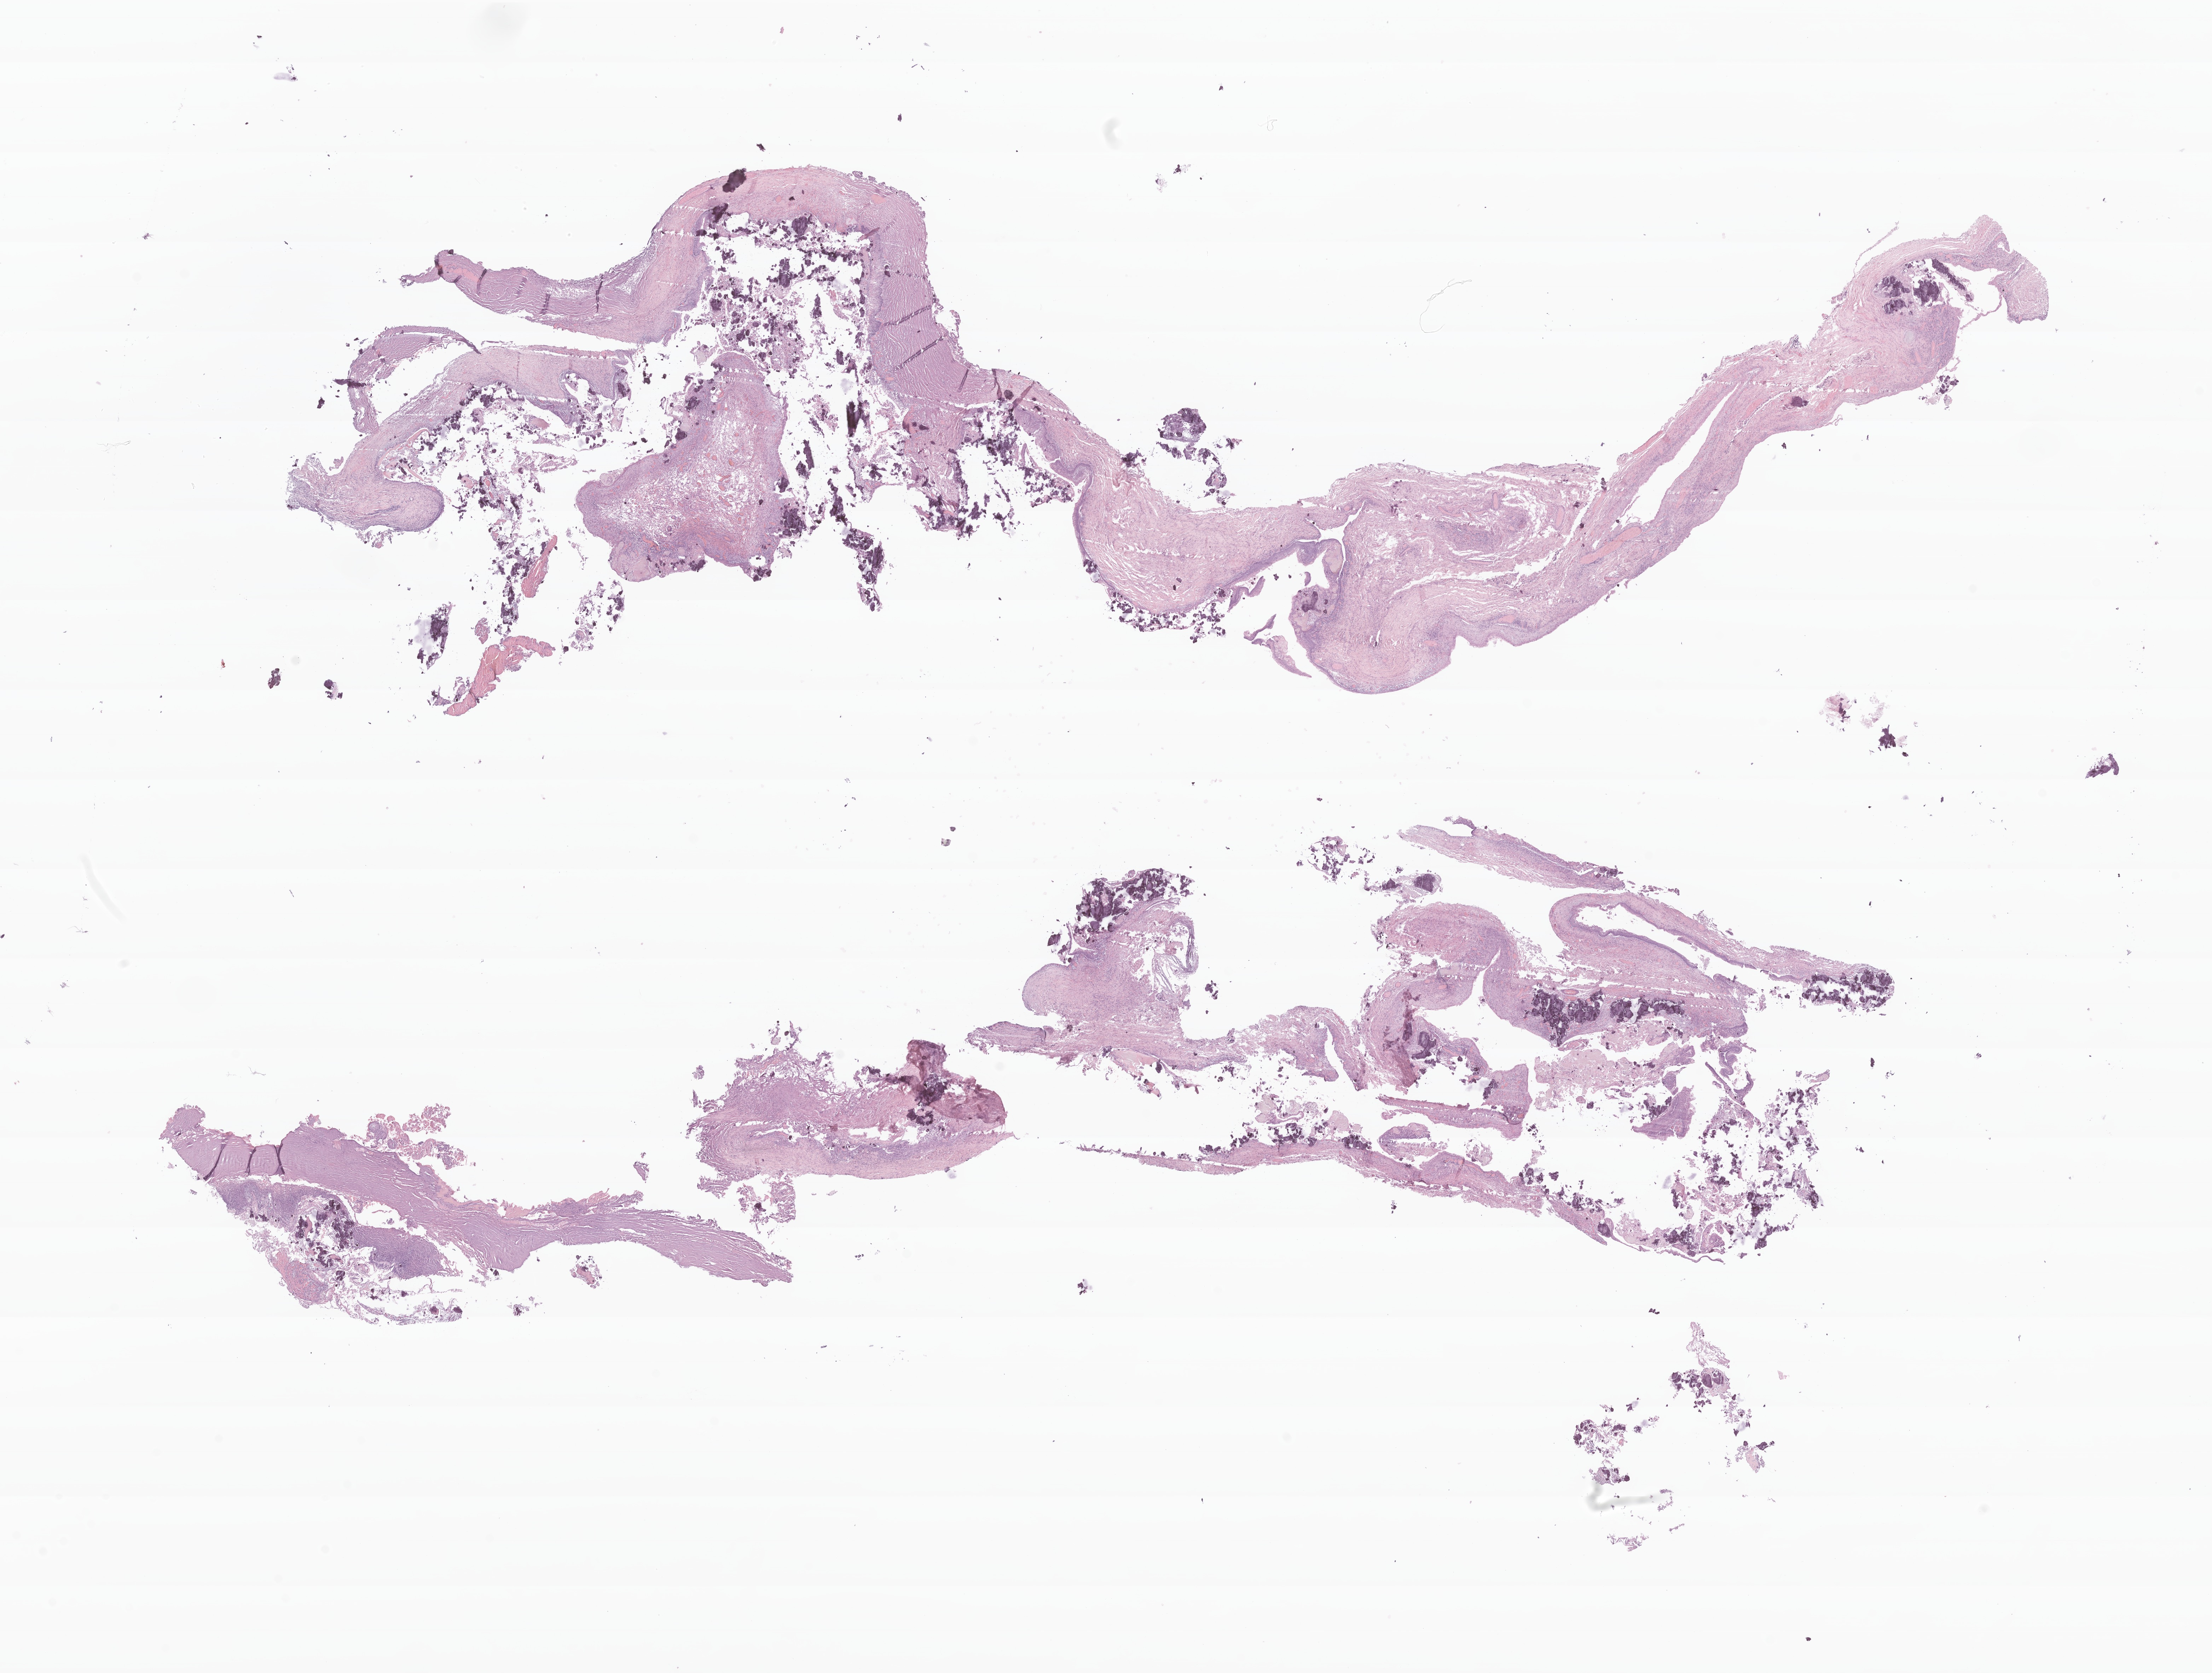
Whole-slide image, haematoxylin and eosin stain of tumor tissue from the brain, shown as a low-resolution overview of the whole scanned area (about 26.3 x 19.9 mm); formalin-fixed, paraffin-embedded (FFPE) tissue. Patient male; age 52 months (4 years 4 months).
Recorded diagnosis: Craniopharyngioma, adamantinomatous.